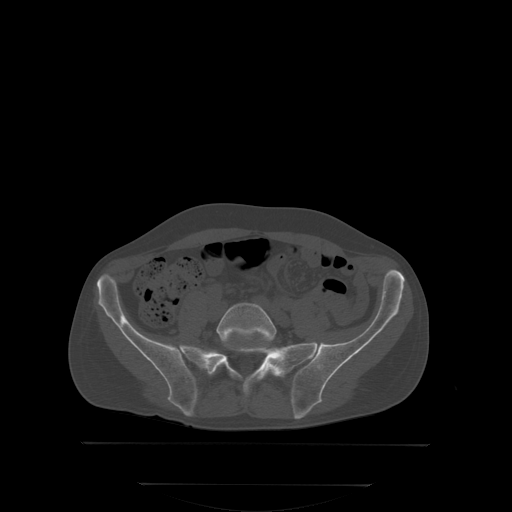
CT including the spine, one axial slice; position 89 of 350 along the scan axis; bone window (W 1800 / L 400 HU); 2.5 mm slice thickness; 512 × 512 image matrix. Male patient, age 58 years. Case-level facts recorded for this patient, not image findings: primary cancer: prostate; vertebrae with lytic lesions (as recorded): L1.
Structures marked on this image (semi-automatically segmented with operator editing):
- L5 vertebra: bounding box [x1, y1, x2, y2] px = [216, 303, 277, 366]